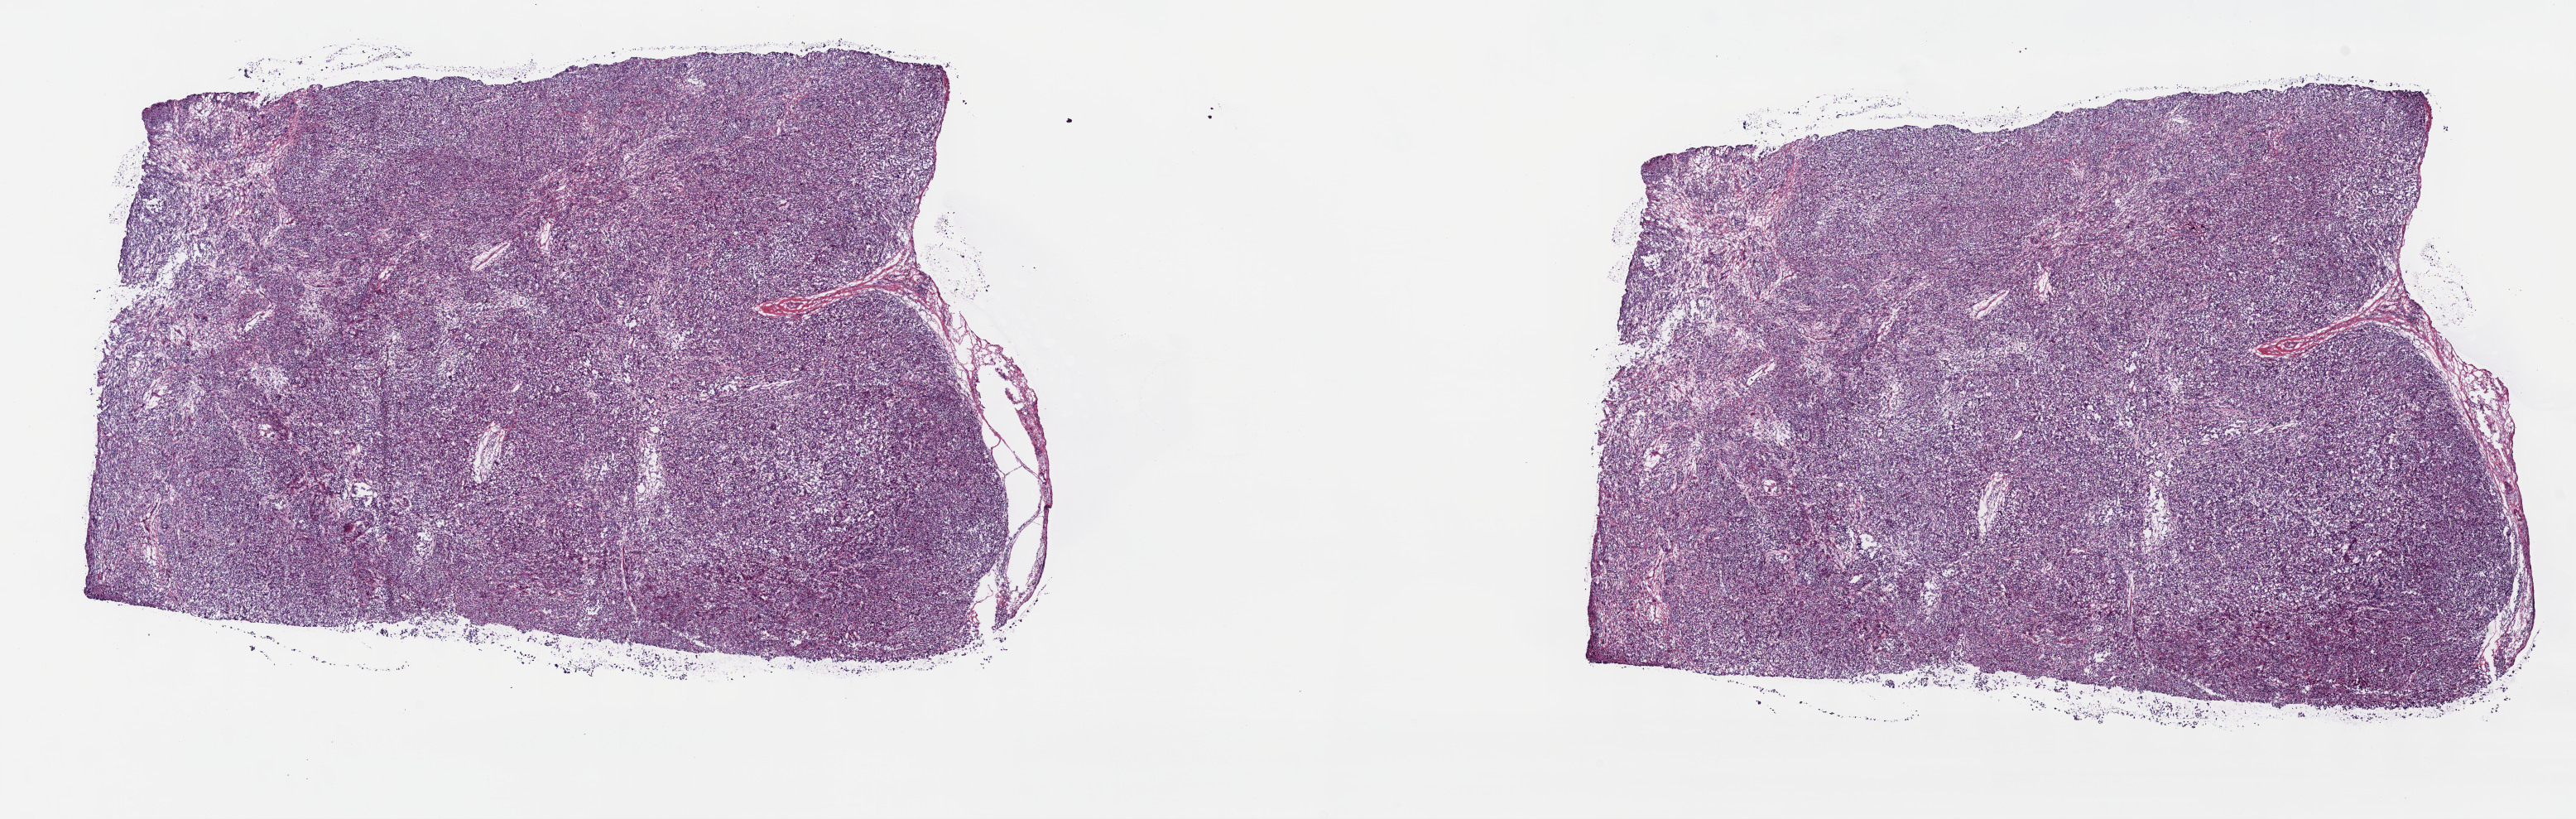
Hematoxylin and eosin (H&E) stained whole-slide image — shown as a low-resolution overview of the whole scanned area (about 25.2 x 8.0 mm); frozen section from the top of the tissue portion; metastatic tumour sample. Male, age 82 years at initial diagnosis. Composition of this section per pathologist review: tumour cells 80%, tumour nuclei 80%, normal cells 0%, stromal cells 20%, necrosis 0%. Infiltration values recorded for this section: lymphocyte infiltration 3%, monocyte infiltration 1%, neutrophil infiltration 2%.
- this section: metastatic tumour tissue
- patient diagnosis: Malignant melanoma, NOS